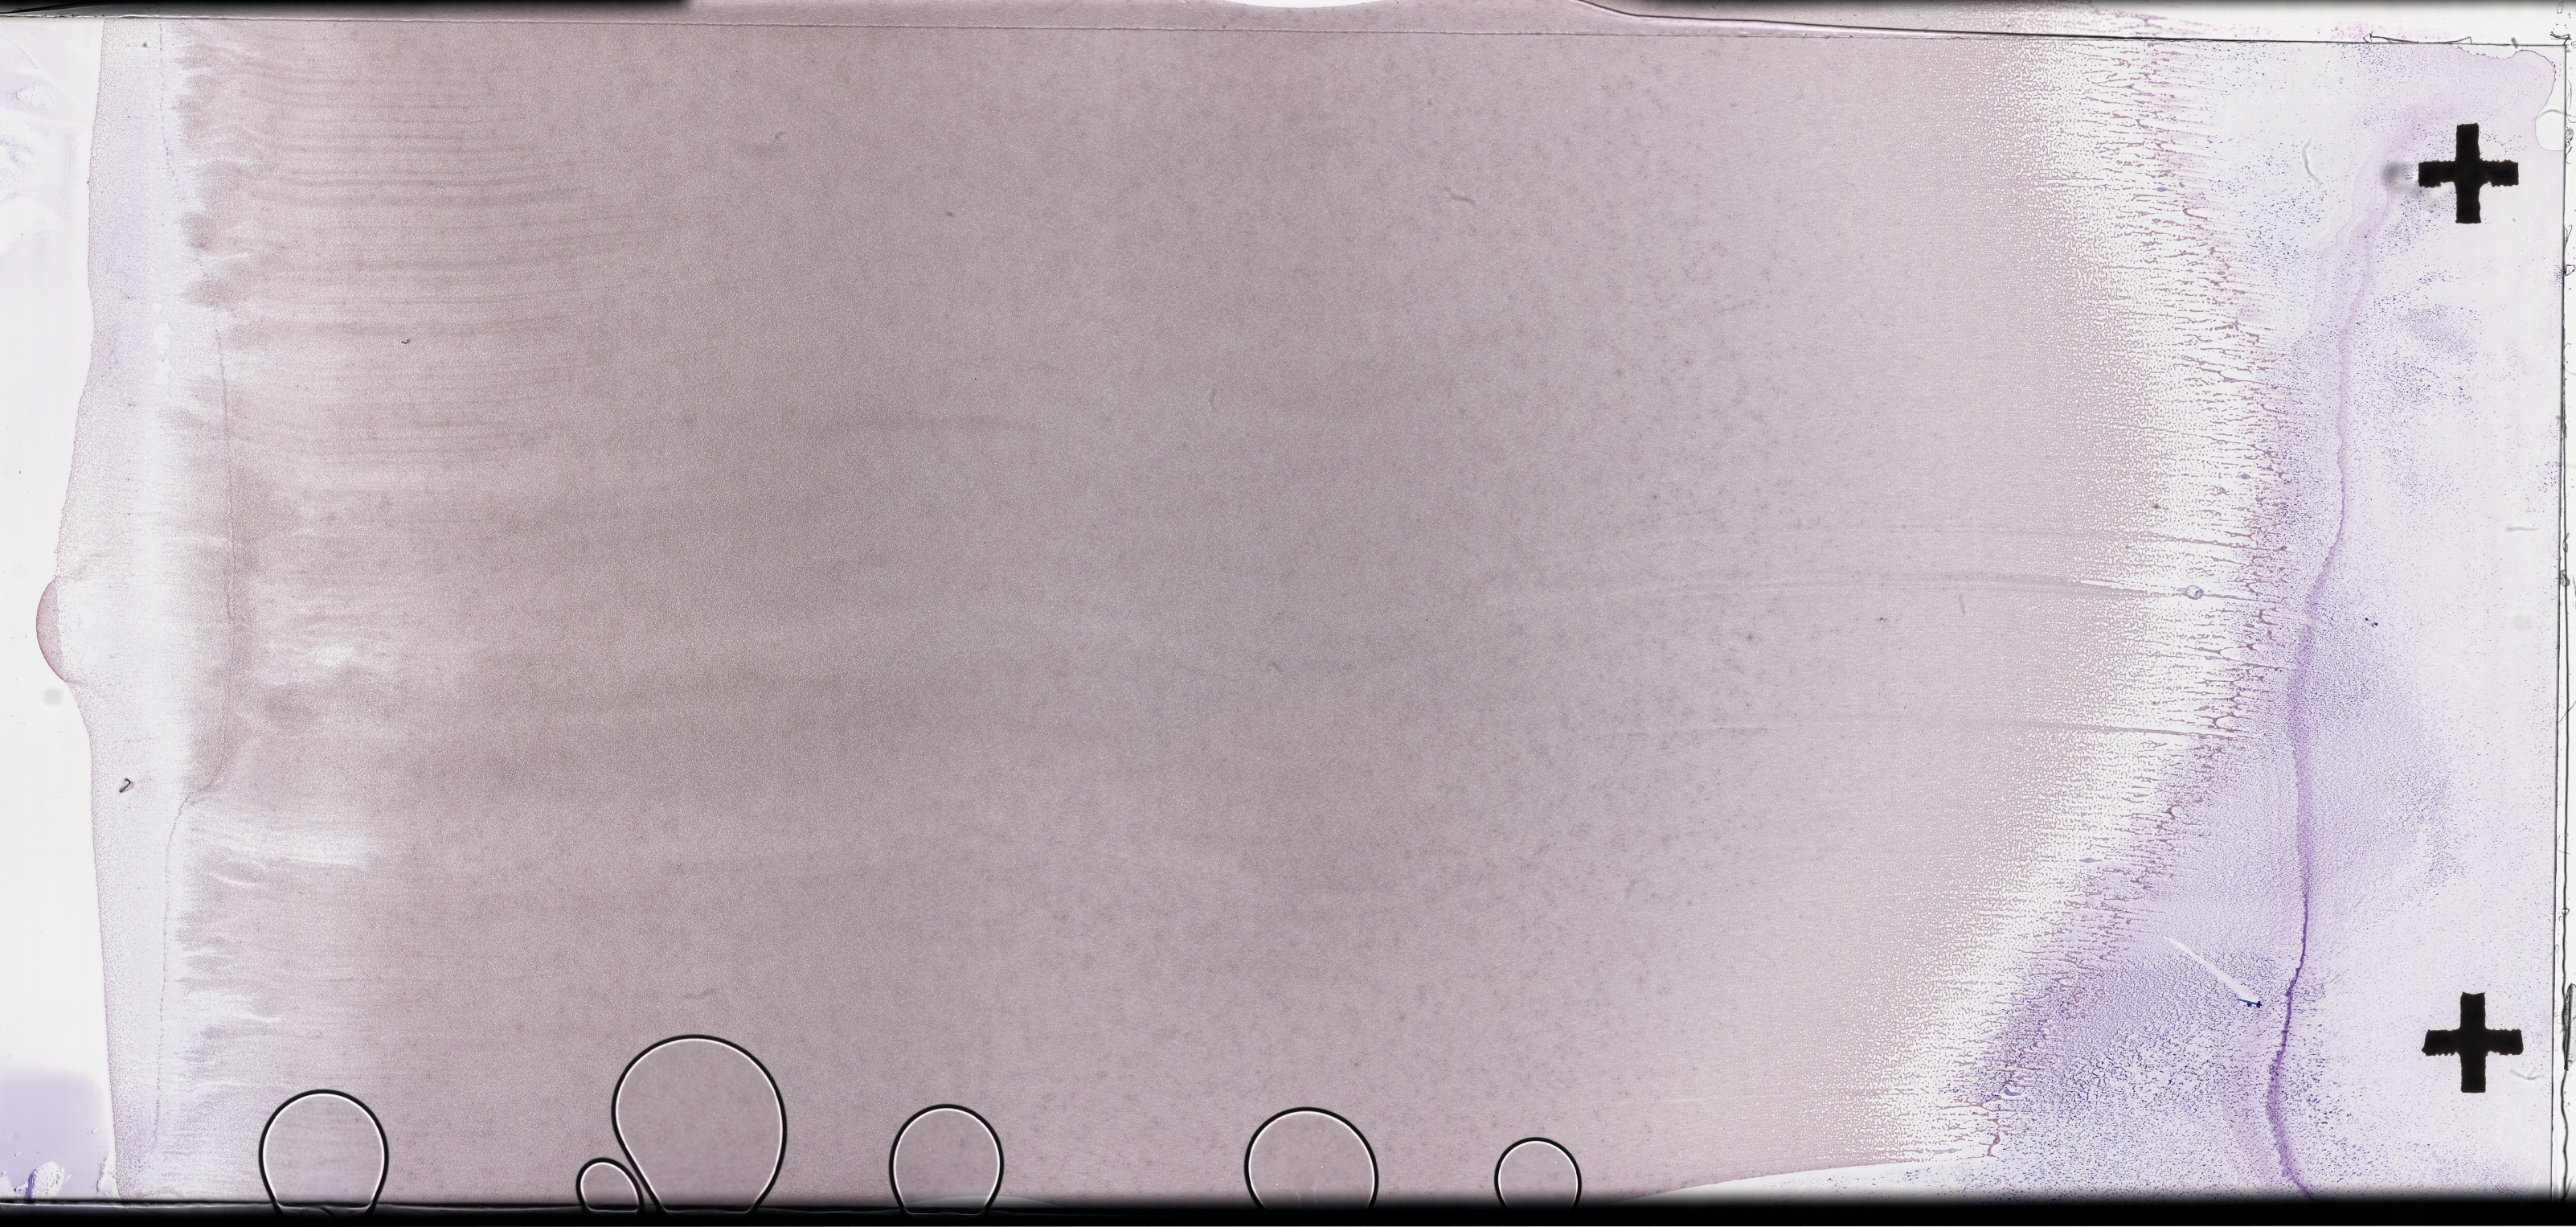
Wright–Giemsa-stained whole blood smear, whole-slide image, a low-resolution overview of the entire scanned area, about 51.8 x 24.6 mm. Specimen time point: collected on treatment. Patient sex: male.
Patient diagnosis: Plasma Cell Myeloma.